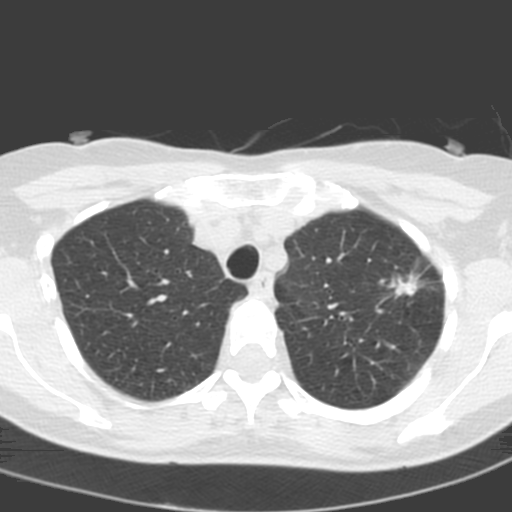
Low-dose screening chest CT, one axial slice. Lung window (W 1500 / L -600 HU). 512 × 512 image matrix.
Structures marked on this image (manually delineated by an expert):
- lesion 1 (tumor, upper lobe of left lung): bounding box <389,273,421,297> (left, top, right, bottom; pixels)